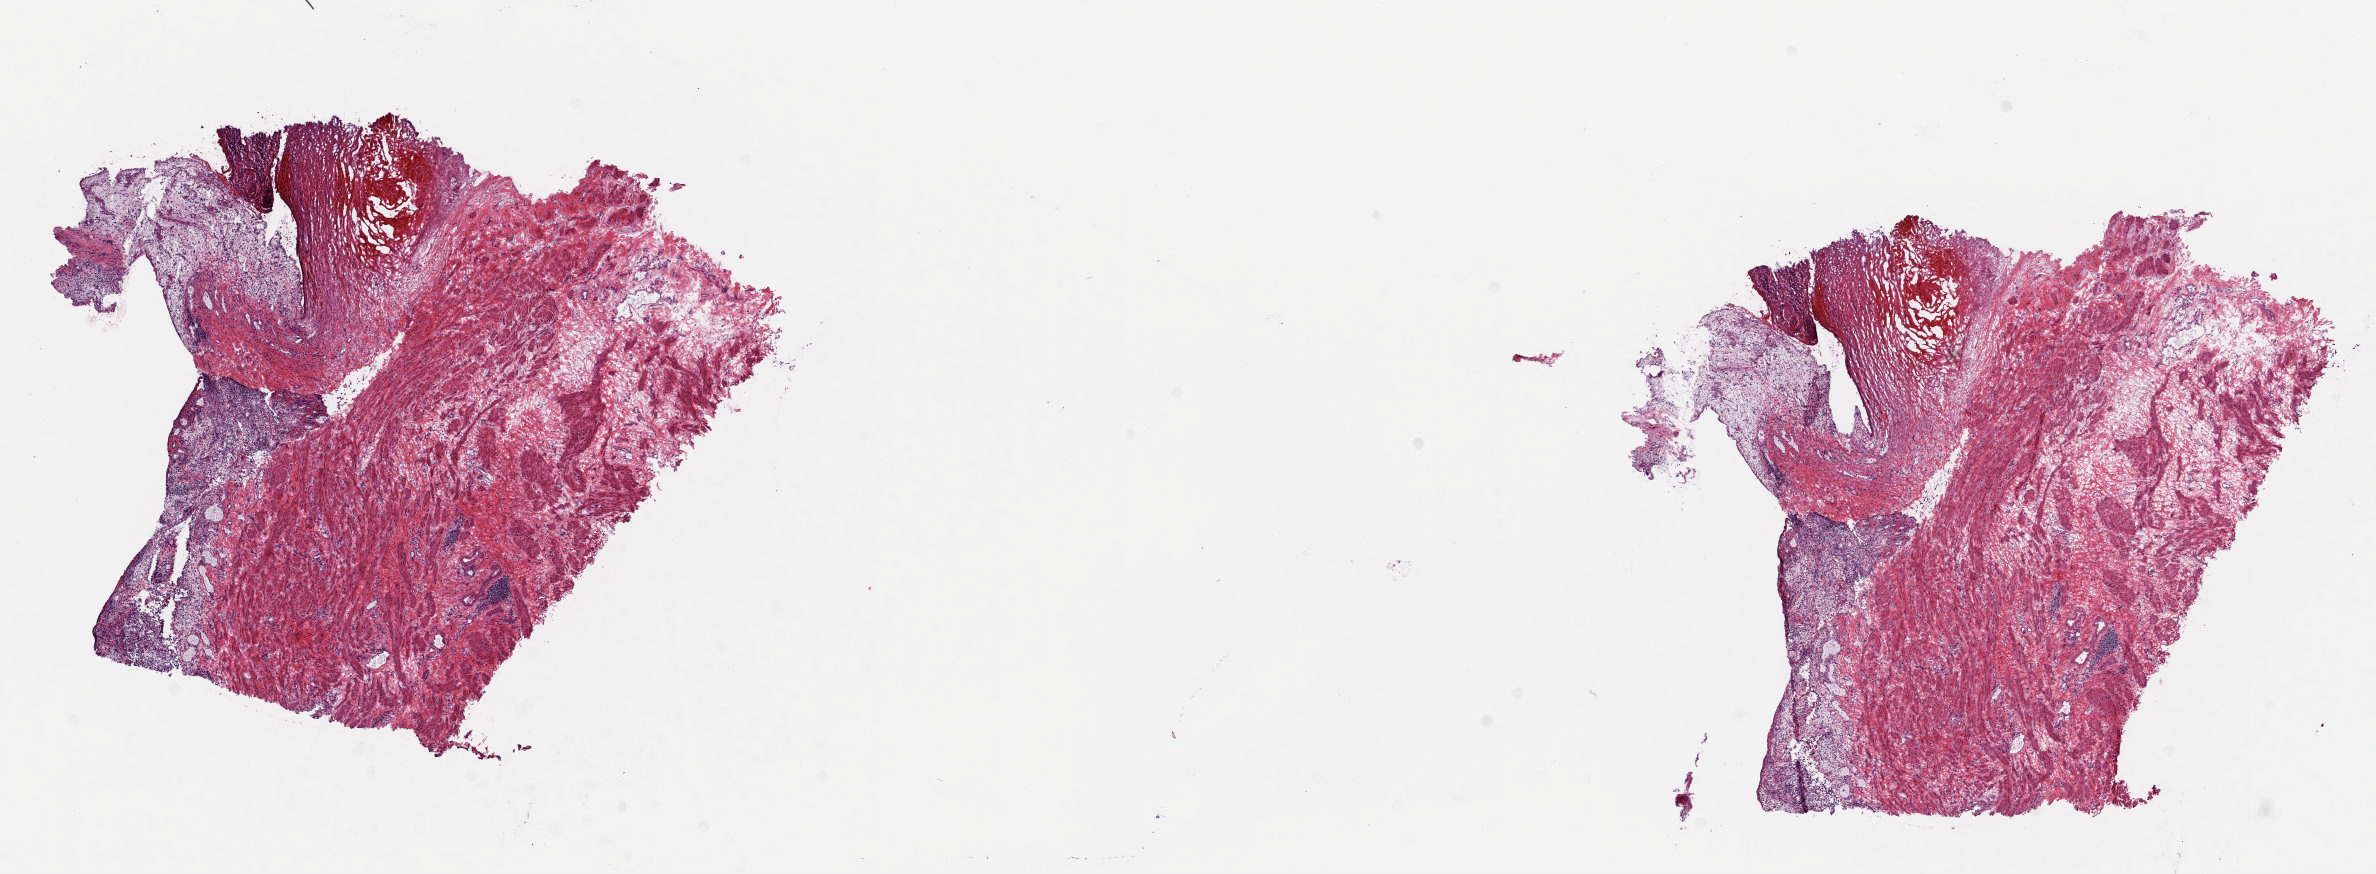
H&E whole-slide image, low-resolution overview of the scanned area, about 18.8 x 6.9 mm (from a 20x scan), frozen section from the top of the tissue portion, solid tissue normal (non-tumour tissue) sample from the uterus. Female, age 53 years at initial diagnosis. Composition of this section per pathologist review: tumour cells 0%, tumour nuclei 0%, normal cells 100%, stromal cells 0%, necrosis 0%. Inflammatory infiltration, as recorded: lymphocyte infiltration 60%, monocyte infiltration 20%, neutrophil infiltration 10%.
* this section: solid tissue normal sample (biorepository sample class)
* patient diagnosis: Serous cystadenocarcinoma, NOS (endometrium)